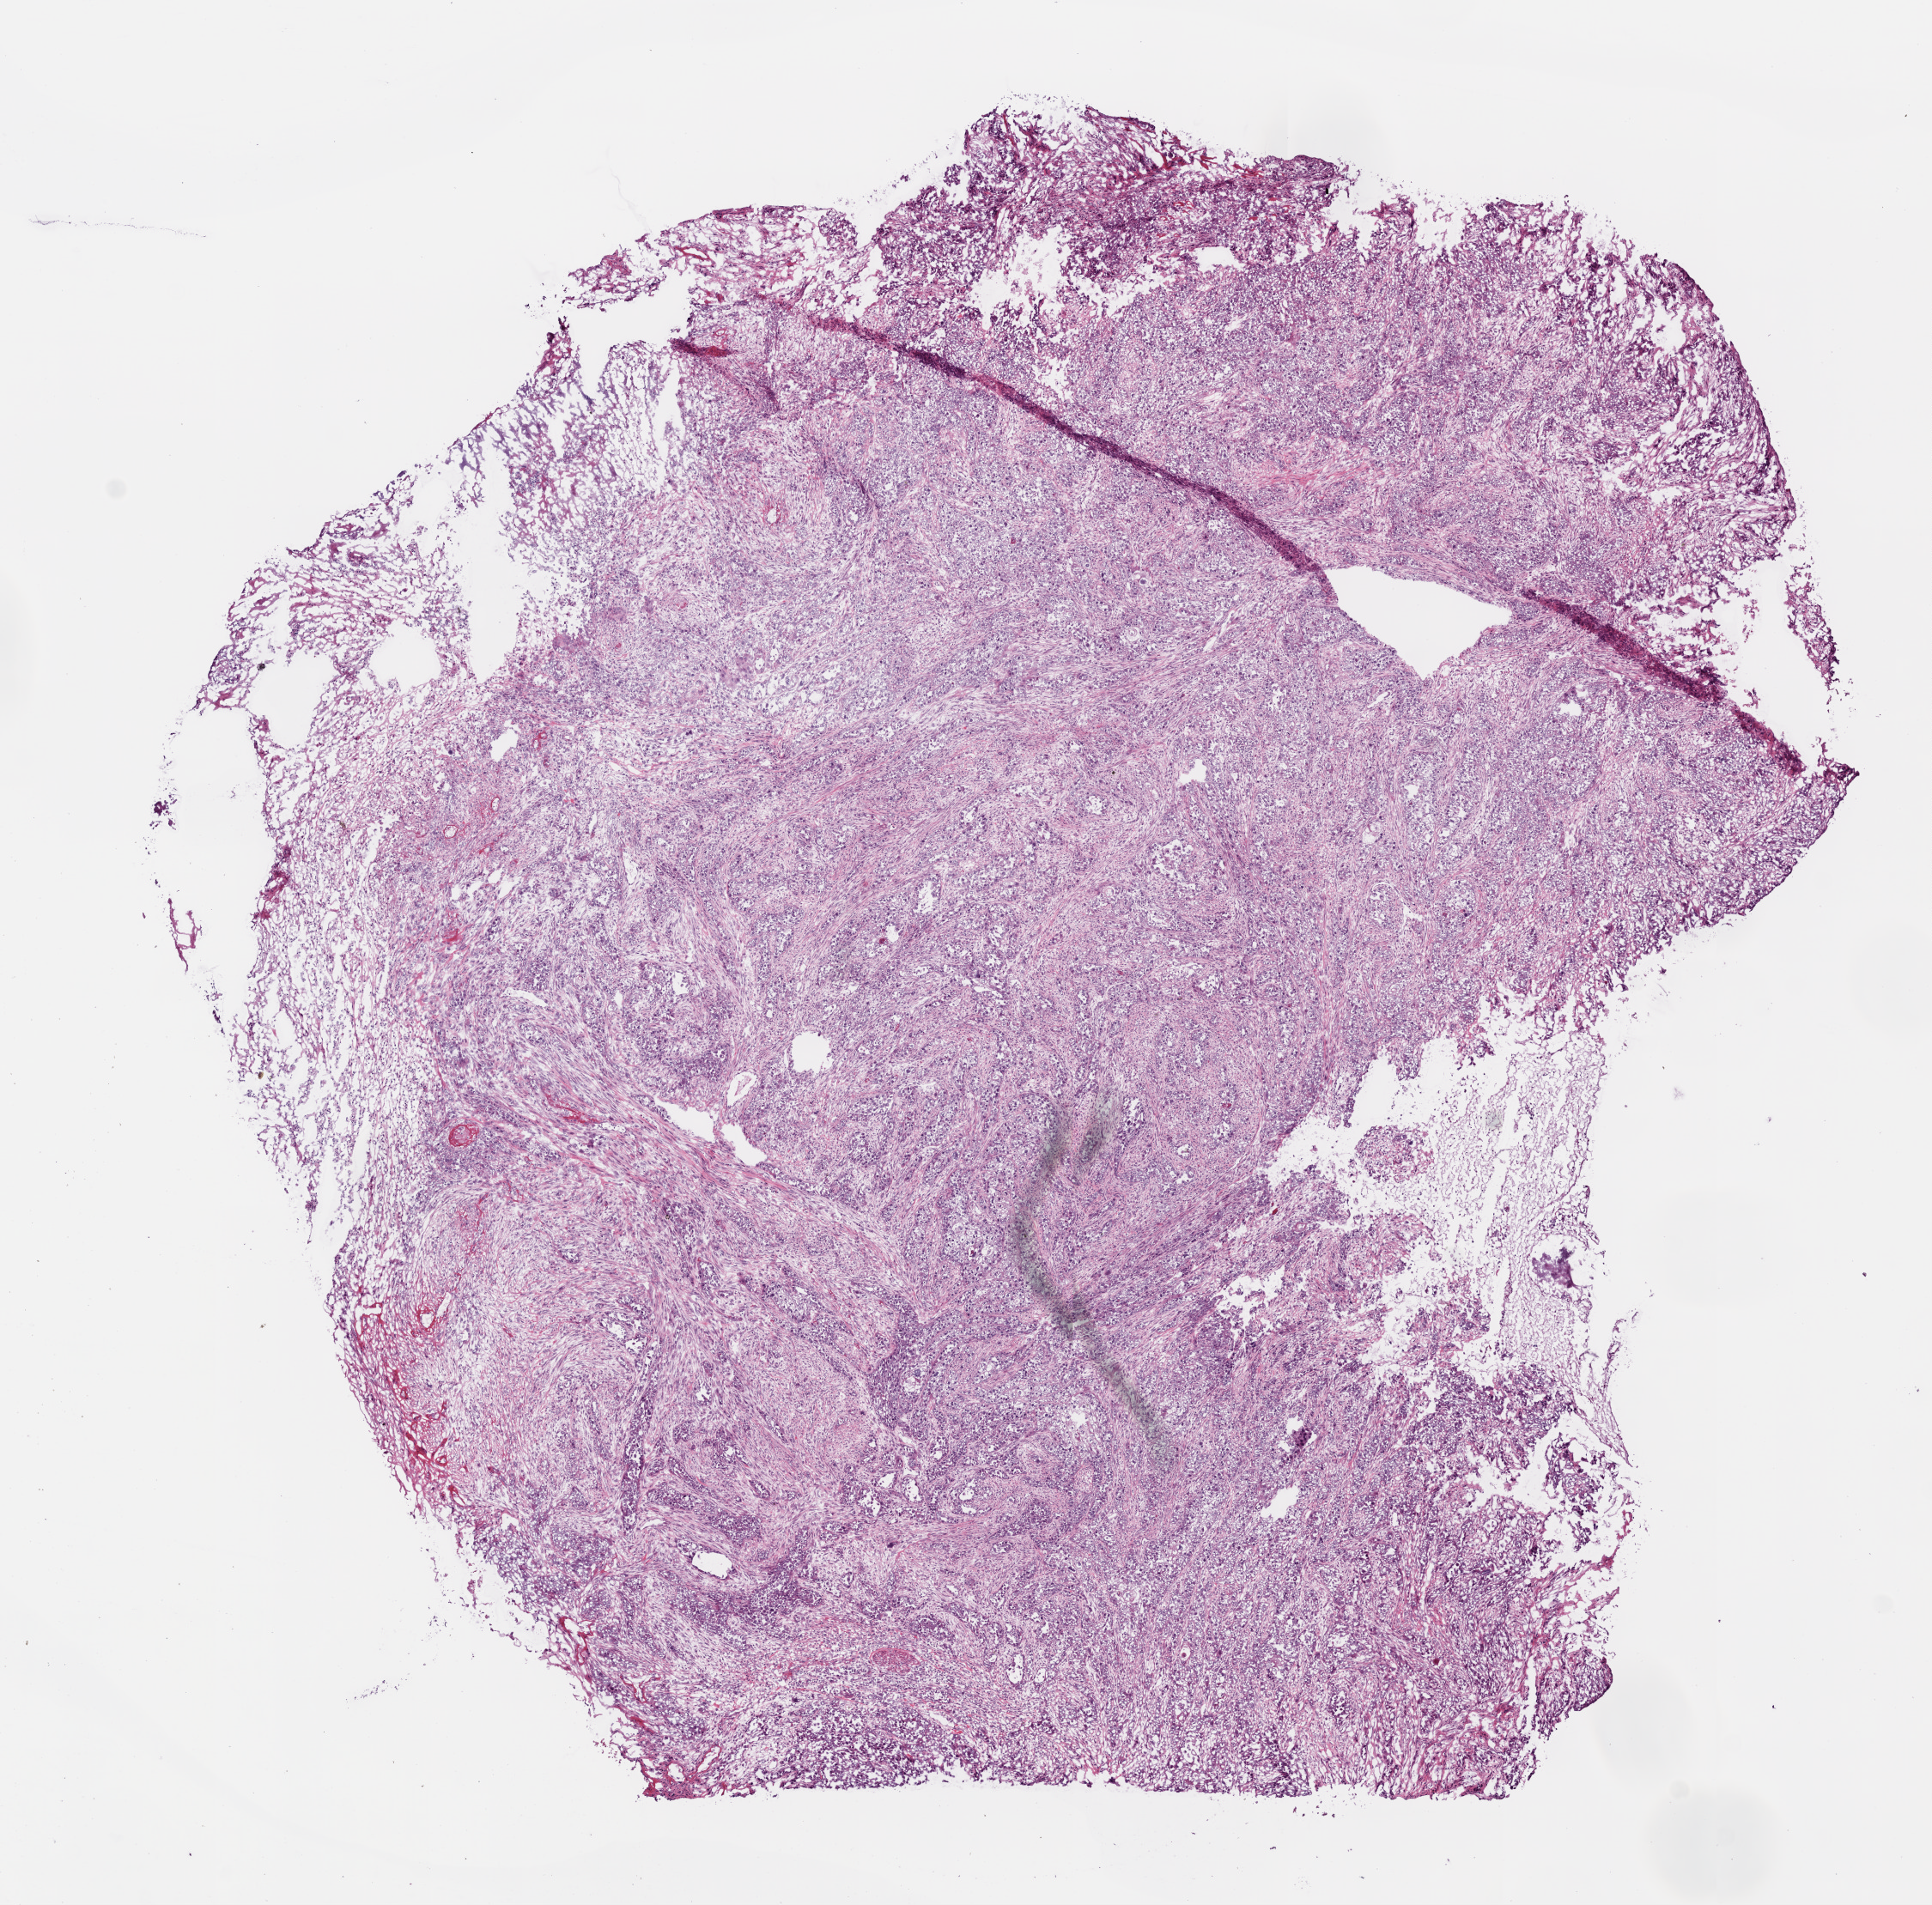
Digitized Hematoxylin and eosin (H&E) stained tissue section (whole slide) — a low-resolution overview of the entire scanned area, about 9.0 x 8.9 mm; frozen section from the bottom of the tissue portion; head and neck, primary tumour sample. Patient: male, age at initial diagnosis 69 years. Histologic grade: G3 (poorly differentiated). Pathologist review of this section (percent, as recorded): tumour cells 87%, tumour nuclei 80%, normal cells 0%, stromal cells 10%, necrosis 3%.
AJCC pathologic stage: IVA. Diagnosis: Squamous cell carcinoma, NOS (tongue, NOS).